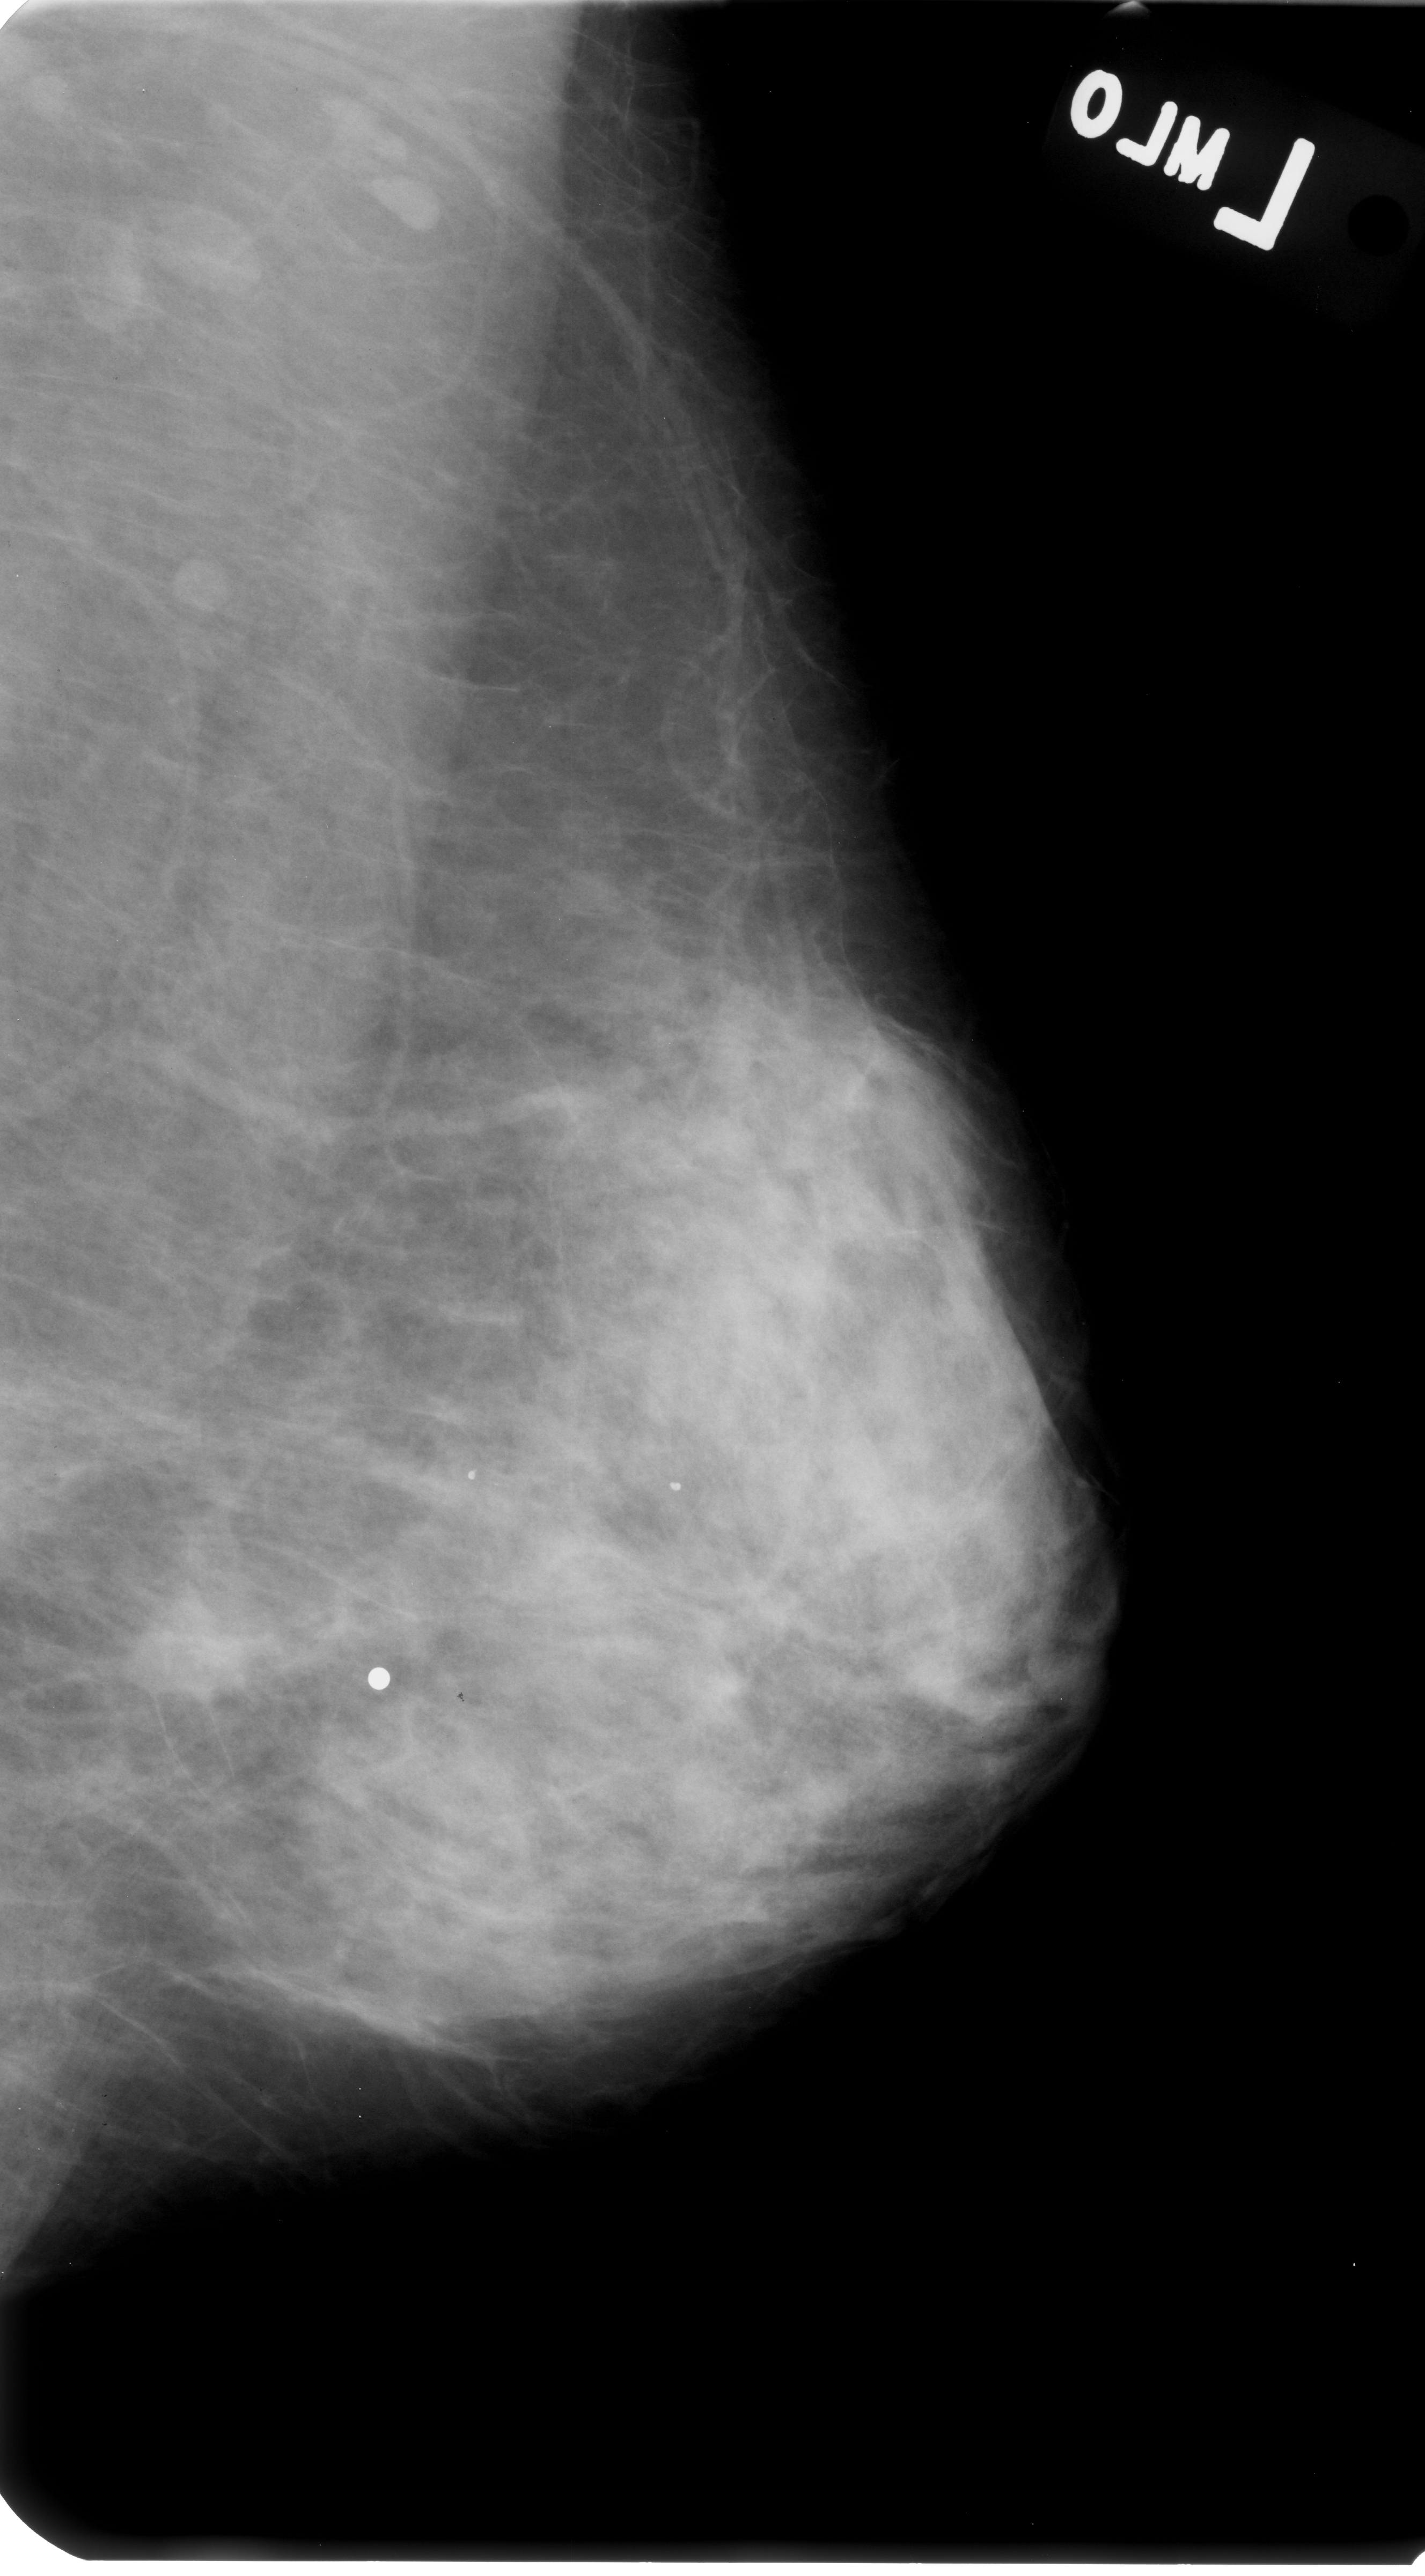
Scanned film-screen mammogram; left breast; mediolateral oblique (MLO) view; breast composition: heterogeneously dense (BI-RADS density category 3 of 4).
Finding: mass, shape irregular / architectural distortion, margins spiculated; BI-RADS assessment category 4; pathology (as recorded): malignant.